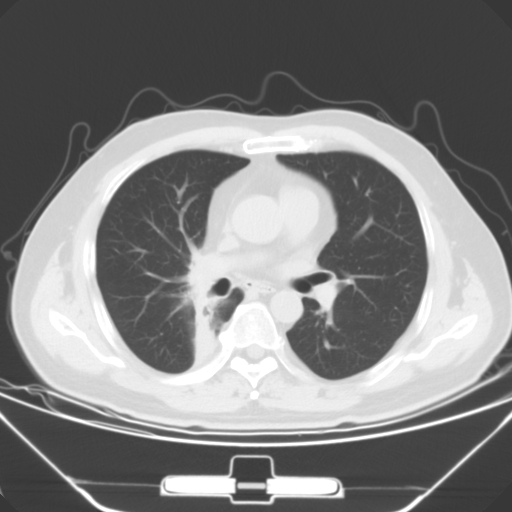
Chest CT, one axial slice; slice 30 of 56 in the series (ordered by position); lung window (W 1500 / L -600 HU); 5 mm slice thickness; 512 × 512 image matrix. Patient: male, 48 years. From the clinical record (not read from this slice): clinical TNM (as recorded): T1a N1 M1c; histopathological grade: G3.
Outlined on this slice (bounding box drawn by a radiologist):
- lung tumour (recorded histology: adenocarcinoma): bounding box <182,249,217,335> (left, top, right, bottom; pixels)